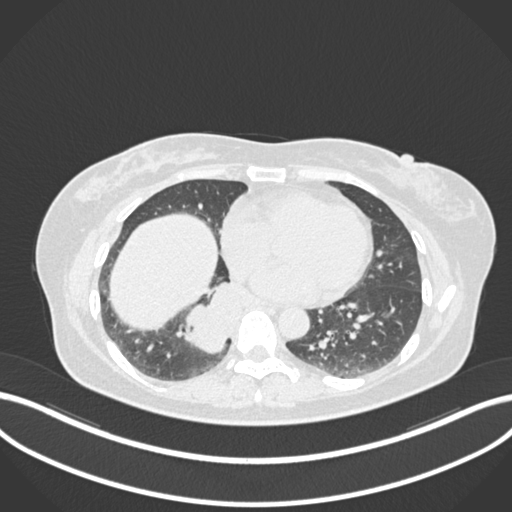
Chest CT, one axial slice. Lung window (W 1500 / L -600 HU). 512 × 512 image matrix, field of view 400 × 400 mm. Patient: female, 54 years. Case-level facts recorded for this patient, not image findings: clinical TNM (as recorded): T4 N0 M0.
Annotated regions visible in this slice (rectangle marked by the reading radiologist):
- lung tumour (recorded histology: adenocarcinoma): bounding box [x1, y1, x2, y2] px = [171, 274, 253, 359]